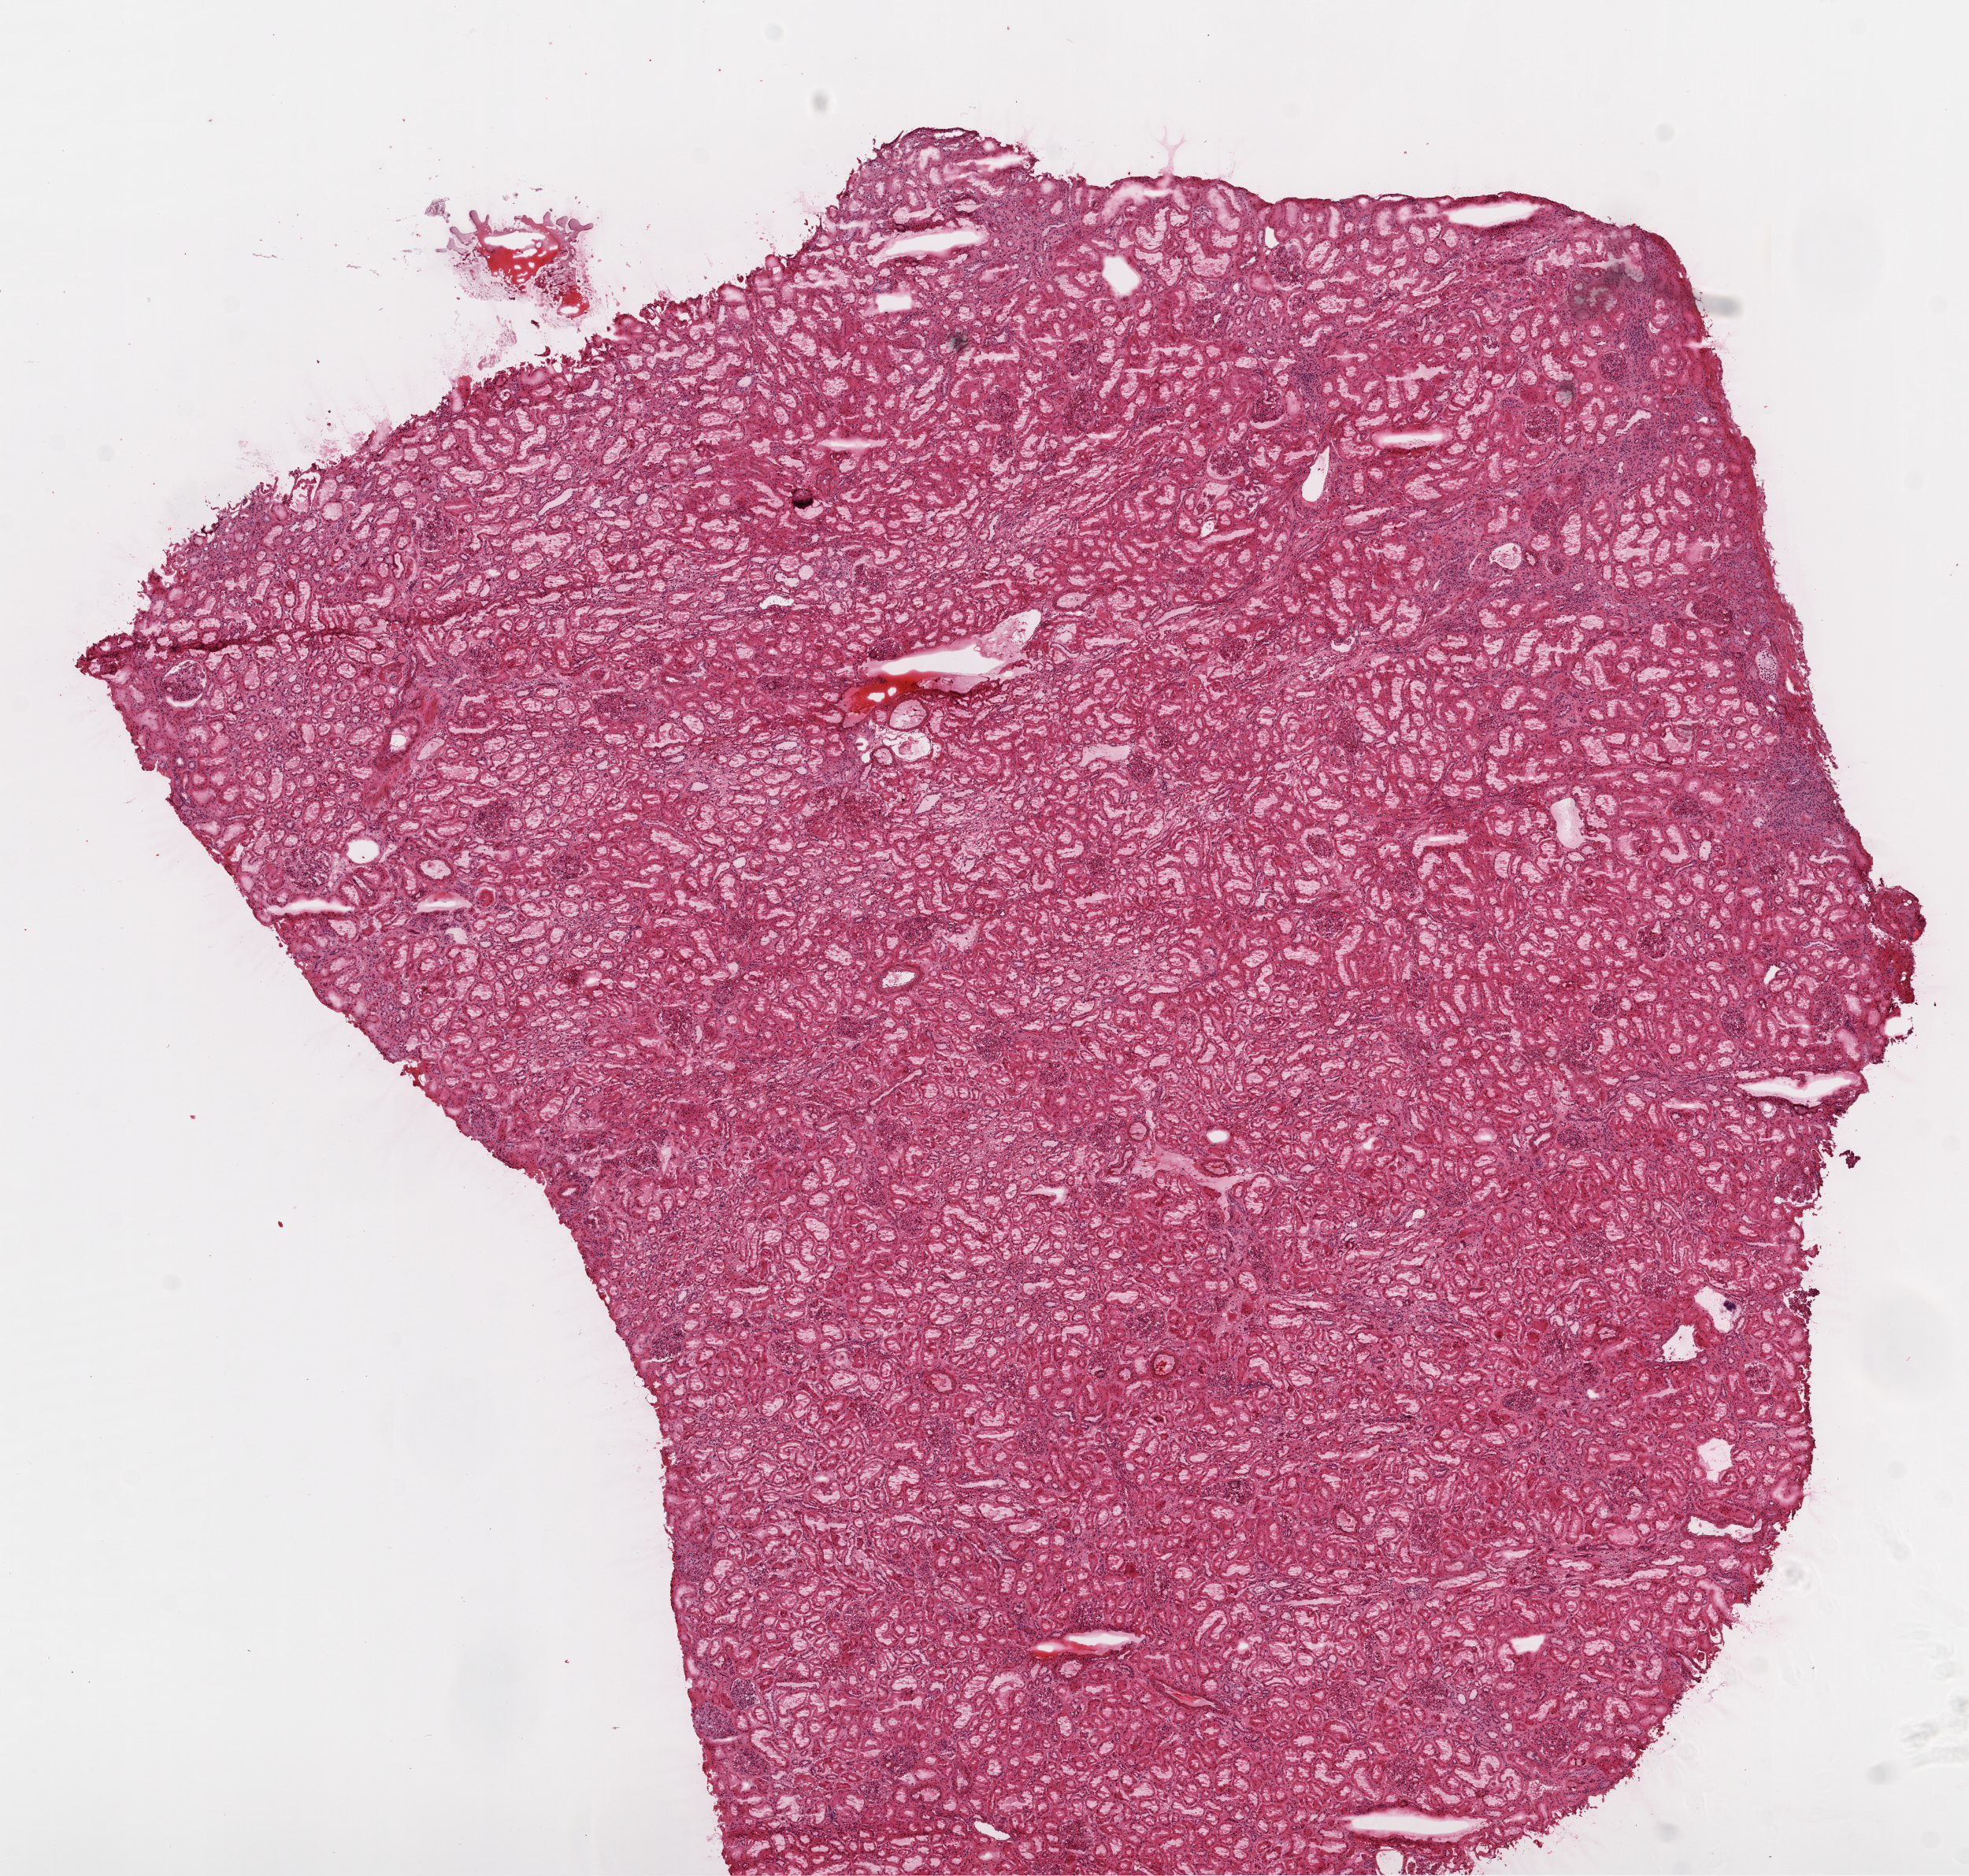
Digitized H&E-stained tissue section (whole slide), shown as a low-resolution overview of the whole scanned area (about 10.0 x 9.6 mm, acquisition: 20x scan), frozen section from the top of the tissue portion, sample: solid tissue normal (non-tumour tissue), kidney. Female, age 70 years at initial diagnosis.
This section: solid tissue normal (non-tumour) sample from the same patient. Patient diagnosis: Clear cell adenocarcinoma, NOS.